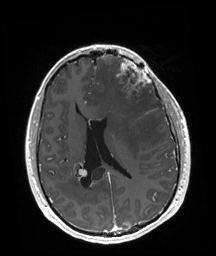
Brain MRI from a brain-tumour surgery series, one axial slice; slice 79 of 192 in the series (ordered by position); T1-weighted post-contrast; 1 mm slice thickness; 216 × 256 image matrix.
Outlined on this slice (manually delineated by an expert):
- tumour: box from (x=116, y=59) to (x=152, y=102) px